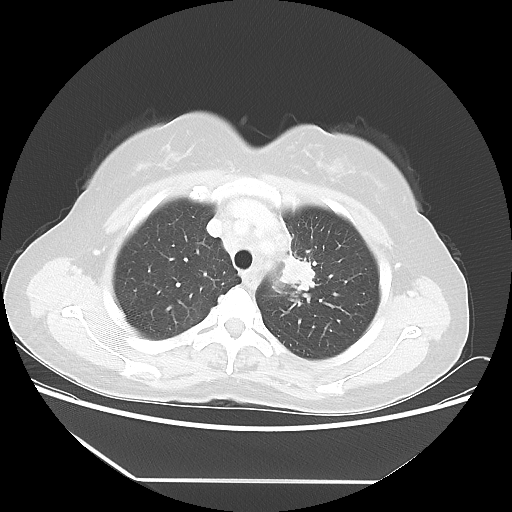
Chest CT, one axial slice; position 41 of 52 along the scan axis; 100 kVp; lung window (W 1500 / L -600 HU); 5 mm slice thickness; 512 × 512 image matrix, field of view 390 × 390 mm. Patient: female, 50 years. Case-level facts recorded for this patient, not image findings: clinical TNM (as recorded): T2 N3 M0.
Annotated regions visible in this slice (rectangle marked by the reading radiologist):
- lung tumour (recorded histology: adenocarcinoma): box from (x=272, y=245) to (x=320, y=296) px